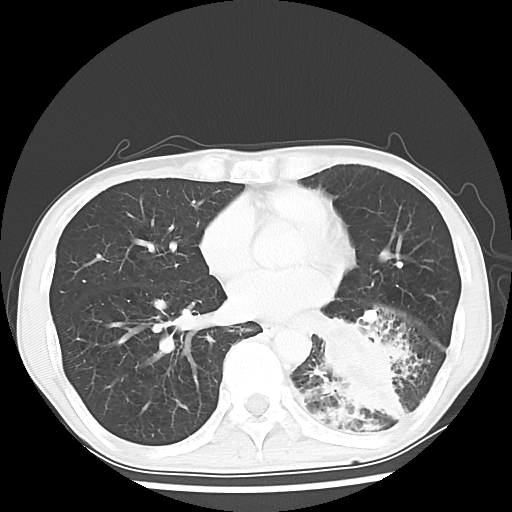
Chest CT, one axial slice; reconstruction kernel LUNG; lung window (W 1500 / L -600 HU); 5 mm slice thickness; 512 × 512 image matrix, field of view 313 × 313 mm. Patient: male, 68 years. Case-level facts recorded for this patient, not image findings: clinical TNM (as recorded): T4 N0 M0.
Structures marked on this image (bounding box drawn by a radiologist):
- lung tumour (recorded histology: squamous cell carcinoma): bounding box [x1, y1, x2, y2] px = [307, 311, 414, 427]